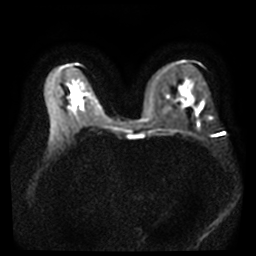
Breast MRI, one axial slice; slice 19 of 40 in the series (ordered by position); diffusion-weighted series; image 2 of 4 stored at this slice position (different b-values; order by instance number); 3 T; 5 mm slice thickness; 256 × 256 image matrix, field of view 360 × 360 mm. Female patient.
Outlined on this slice (outlined manually by an expert reader):
- tumour on diffusion-weighted imaging: bounding box (x1, y1, x2, y2) in pixels: (185, 97, 194, 106)